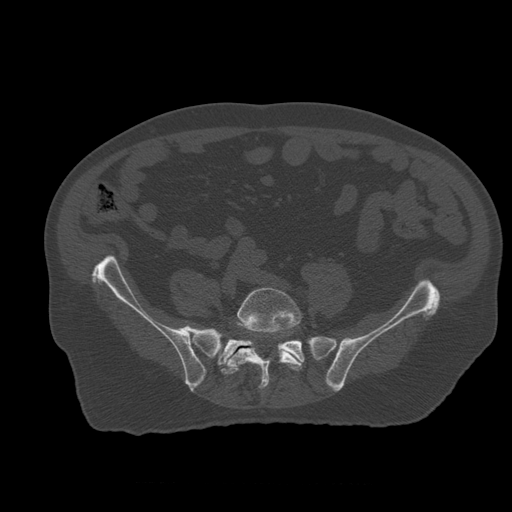
CT including the spine, one axial slice; slice 134 of 399 in the series (ordered by position); reconstruction kernel STANDARD; 120 kVp; bone window (W 1800 / L 400 HU); 512 × 512 image matrix. Patient age 73 years. From the clinical record (not read from this slice): primary cancer: prostate; vertebrae with lytic lesions (as recorded): L2.
Annotated regions visible in this slice (semi-automatically segmented with operator editing):
- L5 vertebra: box from (x=221, y=288) to (x=303, y=390) px